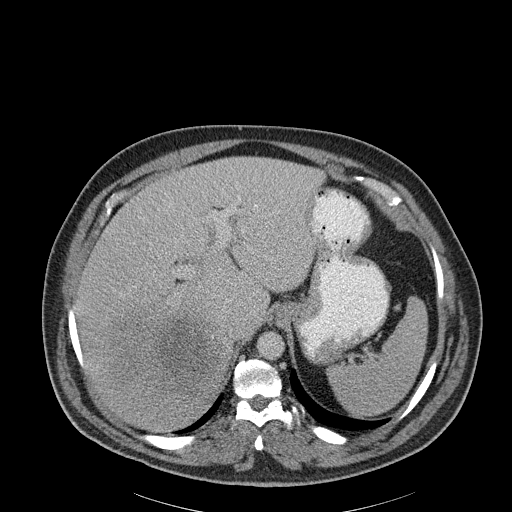
Contrast-enhanced abdominal CT, one axial slice; slice 149 of 186 in the series (ordered by position); reconstruction kernel B30f; 120 kVp; soft-tissue window (W 400 / L 40 HU); 512 × 512 image matrix. Patient: male, 56 years. From the clinical record (not read from this slice): diagnosis: adrenocortical carcinoma; tumour side: right adrenal; tumour size at pathology: 18 cm; Ki-67 index: 2 %; stage (as recorded): 3.
Annotated regions visible in this slice (semi-automatic segmentation, software-assisted and operator-edited):
- mass: bounding box (x1, y1, x2, y2) in pixels: (104, 316, 220, 387)